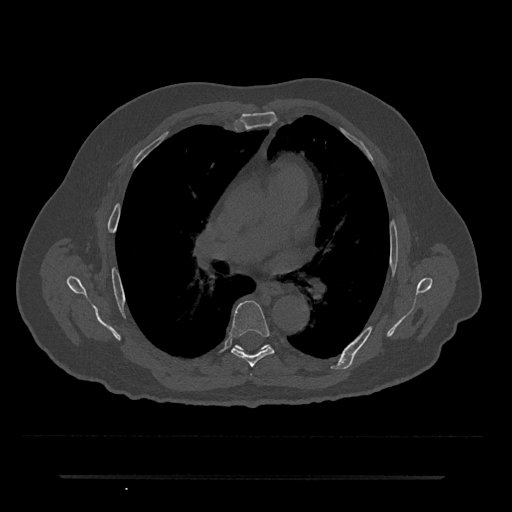
CT including the spine, one axial slice. Slice 427 of 797 in the series (ordered by position). 120 kVp. Bone window (W 1800 / L 400 HU). 512 × 512 image matrix, field of view 437 × 437 mm. Male patient, age 69 years. From the clinical record (not read from this slice): primary cancer: prostate.
Structures marked on this image (semi-automatically segmented with operator editing):
- T6 vertebra: bounding box [x1, y1, x2, y2] px = [230, 301, 274, 367]
- T7 vertebra: [236, 346, 241, 349]